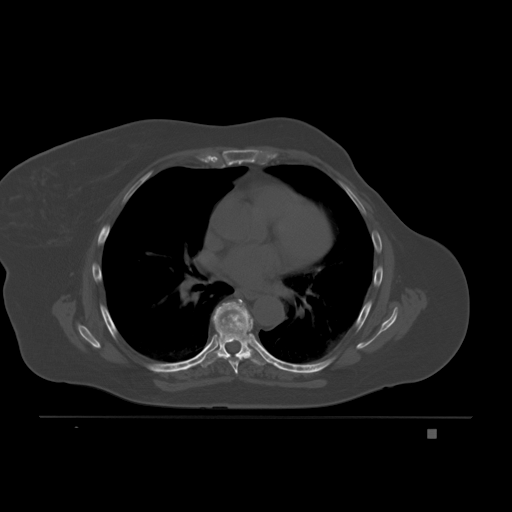
CT including the spine, one axial slice; position 131 of 221 along the scan axis; bone window (W 1800 / L 400 HU); 512 × 512 image matrix, field of view 474 × 474 mm. Patient: female, 63 years. Case-level facts recorded for this patient, not image findings: primary cancer: breast.
Structures marked on this image (semi-automatically segmented with operator editing):
- T6 vertebra: bounding box (x1, y1, x2, y2) in pixels: (225, 335, 248, 374)
- T7 vertebra: (201, 299, 266, 368)